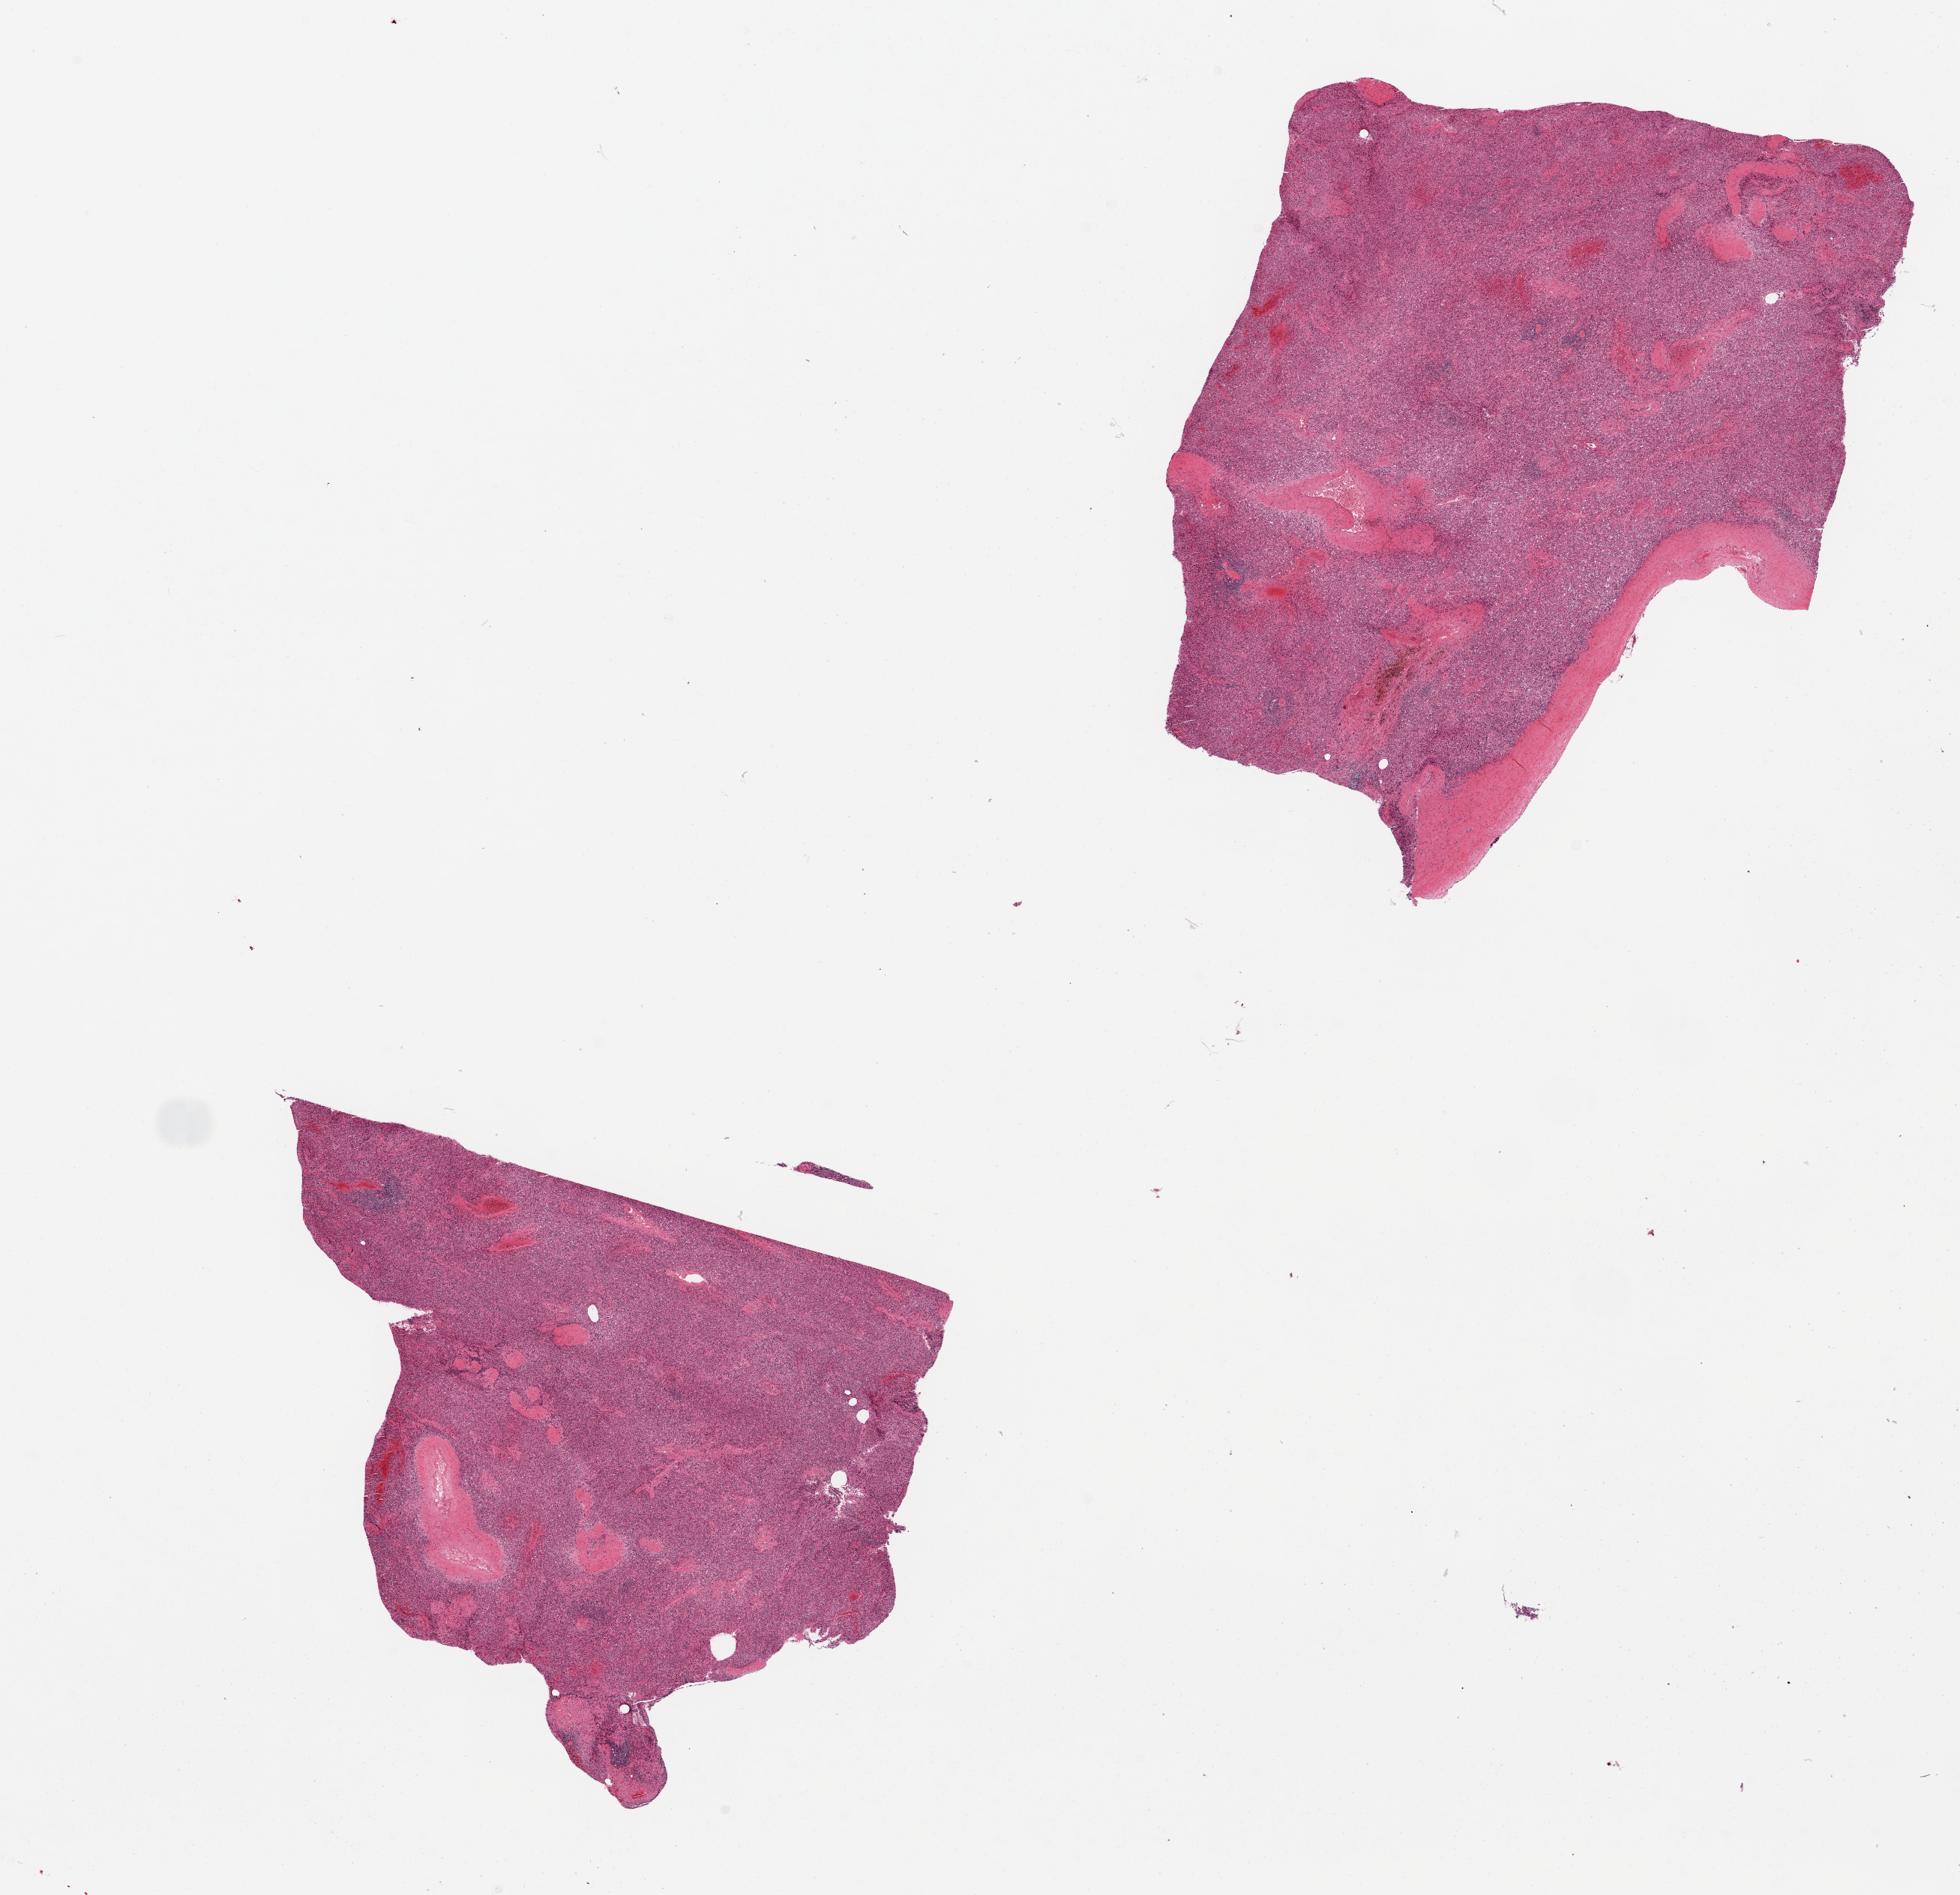
Whole-slide image, H&E stain, brightfield — a low-resolution overview of the entire scanned area, about 20.7 x 20.0 mm; PAXgene-fixed, paraffin-embedded tissue; section of spleen (target tissue); tissue donor sample.
• reviewer comment on this tissue sample: 2 pieces, moderate congestion